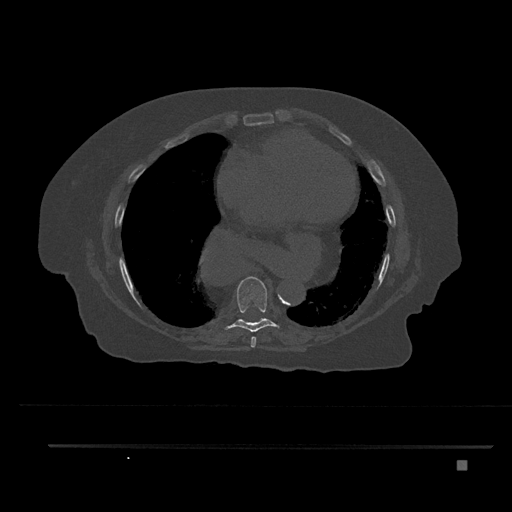
CT including the spine, one axial slice. Position 443 of 797 along the scan axis. Reconstruction kernel Br40s/3. Bone window (W 1800 / L 400 HU). 0.5 mm slice thickness. 512 × 512 image matrix. Female patient, age 76 years. From the clinical record (not read from this slice): primary cancer: lung.
Annotated regions visible in this slice (semi-automatically segmented with operator editing):
- T7 vertebra: bounding box [x1, y1, x2, y2] px = [251, 336, 256, 348]
- T8 vertebra: [222, 277, 281, 332]